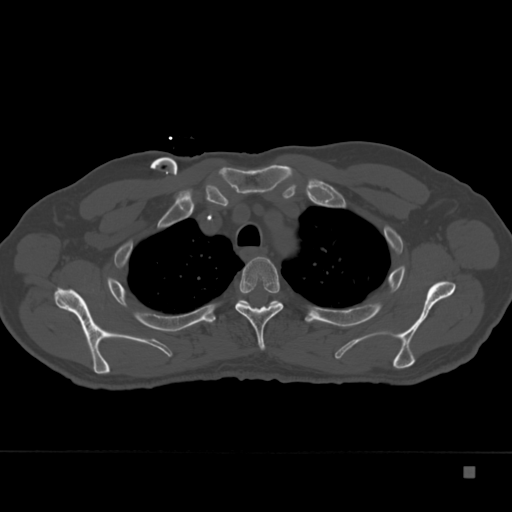
CT including the spine, one axial slice. Position 284 of 332 along the scan axis. Reconstruction kernel Br40s. Bone window (W 1800 / L 400 HU). 512 × 512 image matrix, field of view 389 × 389 mm. Male patient, age 72 years. Case-level facts recorded for this patient, not image findings: primary cancer: skeletal.
Outlined on this slice (semi-automatic segmentation, software-assisted and operator-edited):
- T3 vertebra: box from (x=235, y=256) to (x=283, y=351) px
- T4 vertebra: (x=238, y=300)–(x=279, y=306)